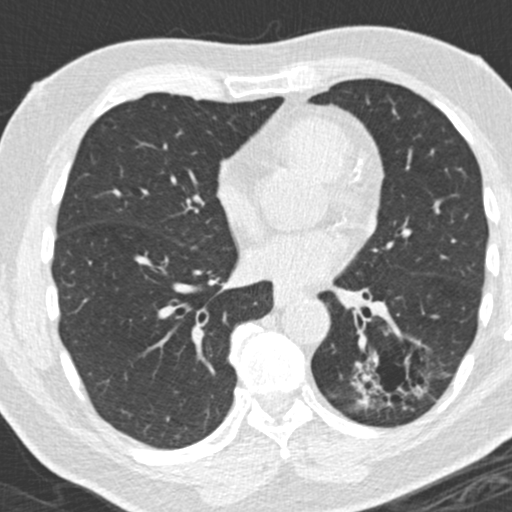
Low-dose screening chest CT, axial slice; third annual screen; lung window (W 1500 / L -600 HU); 2 mm slice thickness; standard (soft-tissue) reconstruction kernel (B30f). Male participant, aged 66 years at enrolment. Former smoker at enrolment.
Lesion marked by an expert reader, bounding box (x1, y1, x2, y2) in pixels: (356, 347, 427, 428). Screening reader's record for this exam (one nodule recorded; not confirmed to be the boxed lesion): non-calcified nodule or mass ≥4 mm, left lower lobe, 31 × 24 mm, spiculated (stellate) margins, pre-existing on the prior screen: yes; interval growth: yes. Later outcome: lung cancer diagnosed 56 days after this screen — adenocarcinoma, NOS, left lower lobe, poorly differentiated (G3), stage IB (AJCC 6th edition), 38 mm at pathology.